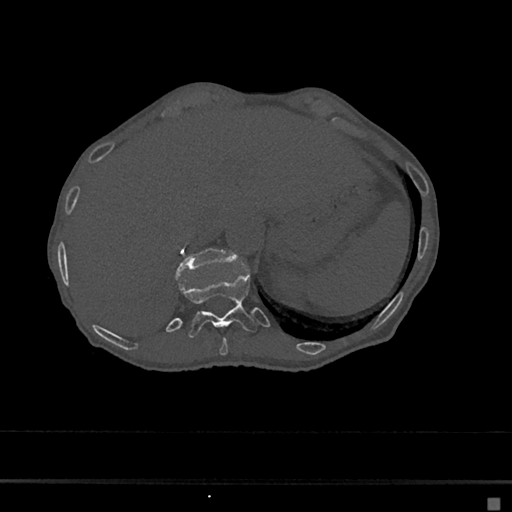
CT including the spine, one axial slice; position 173 of 797 along the scan axis; 120 kVp; bone window (W 1800 / L 400 HU); 0.5 mm slice thickness; 512 × 512 image matrix, field of view 360 × 360 mm. Female patient, age 68 years. From the clinical record (not read from this slice): primary cancer: renal.
Outlined on this slice (semi-automatically segmented with operator editing):
- T10 vertebra: bounding box <219,337,228,356> (left, top, right, bottom; pixels)
- T11 vertebra: <175,273,257,338>
- T12 vertebra: <175,247,236,278>